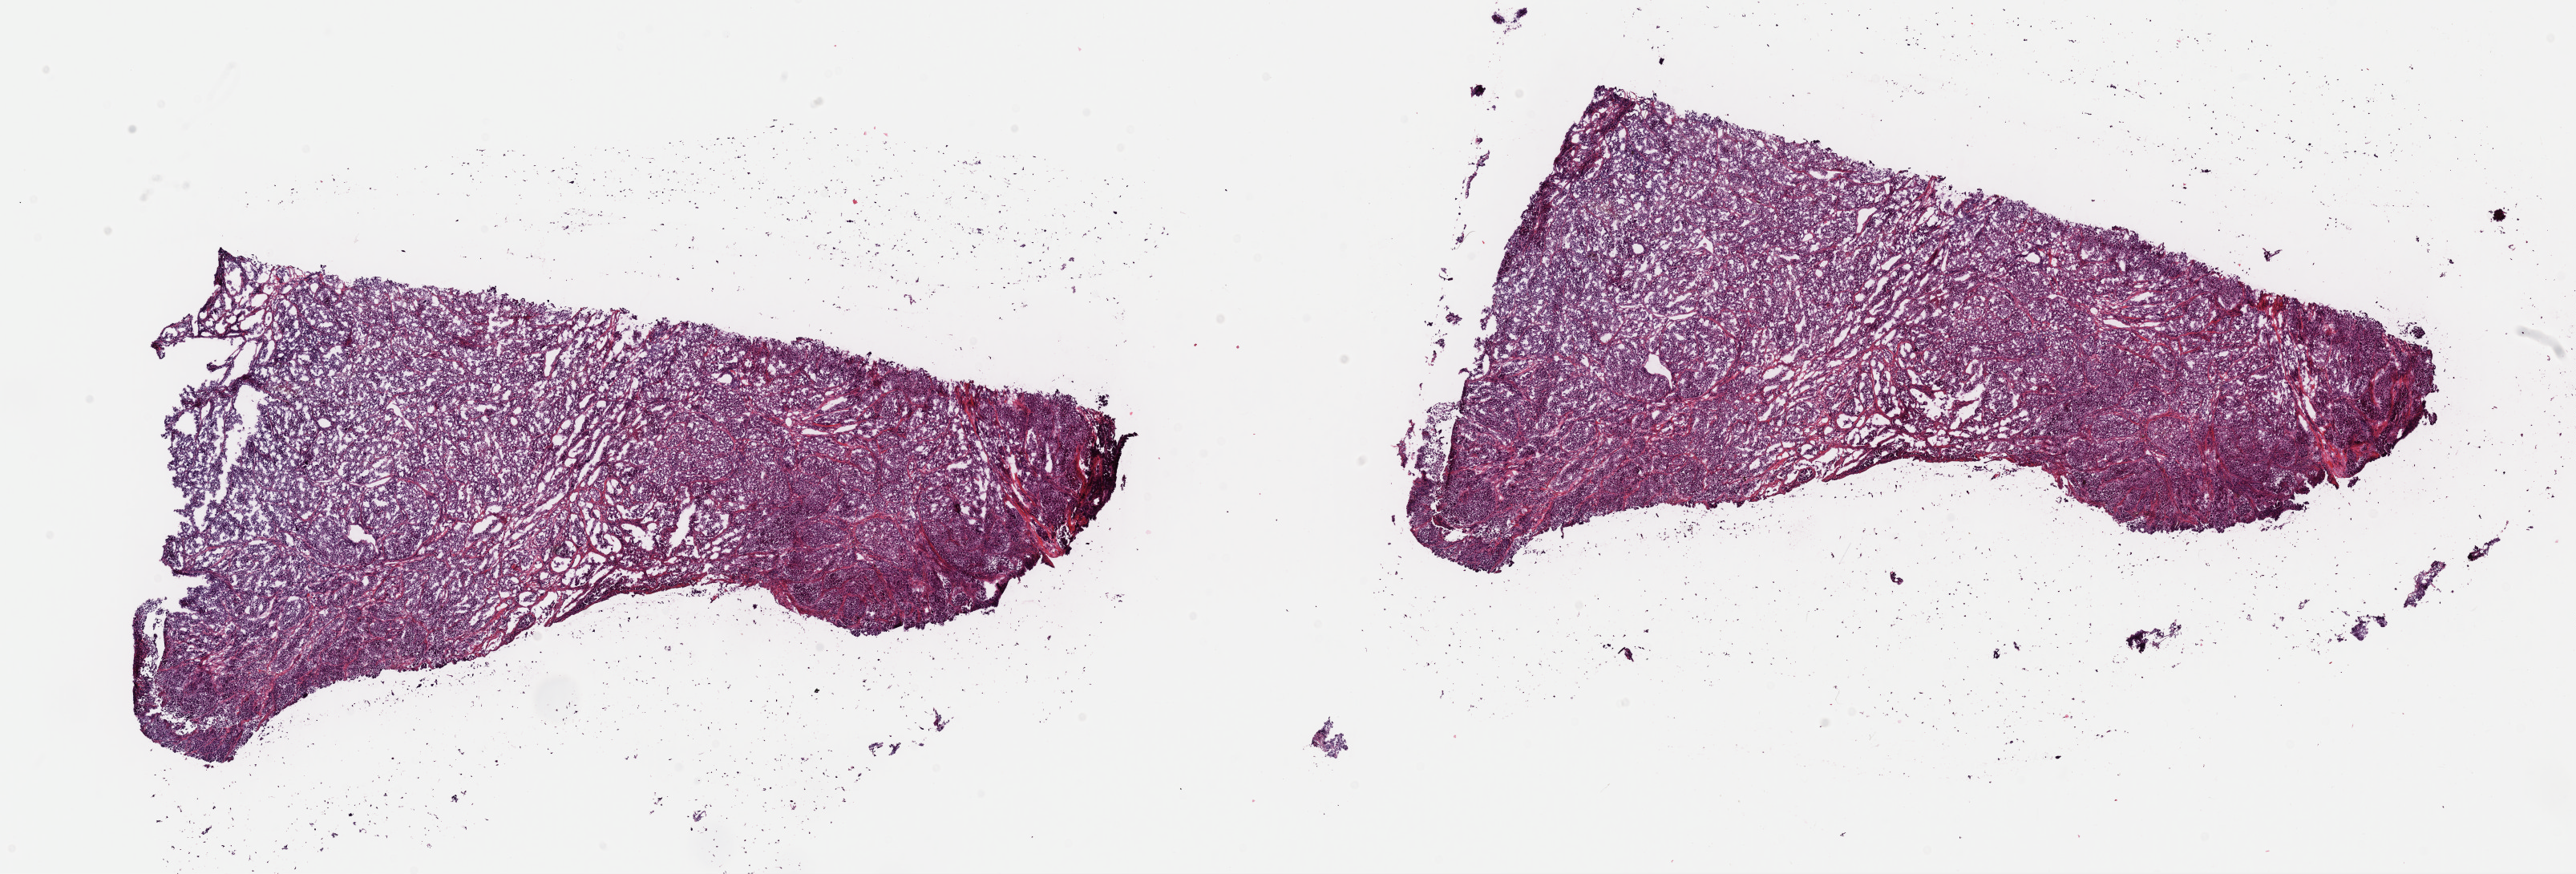
Whole-slide histology image, Hematoxylin and eosin (H&E) stained — a low-resolution overview of the entire scanned area, about 25.4 x 8.6 mm. Frozen section from the top of the tissue portion. Metastatic tumour sample. Female patient; age at initial diagnosis 30 years. Slide review estimates, as recorded: tumour cells 88%, tumour nuclei 90%, normal cells 0%, stromal cells 10%, necrosis 2%. Inflammatory infiltration, as recorded: lymphocyte infiltration 0%, monocyte infiltration 0%, neutrophil infiltration 0%.
This section: metastatic tumour tissue. Patient diagnosis: Malignant melanoma, NOS.